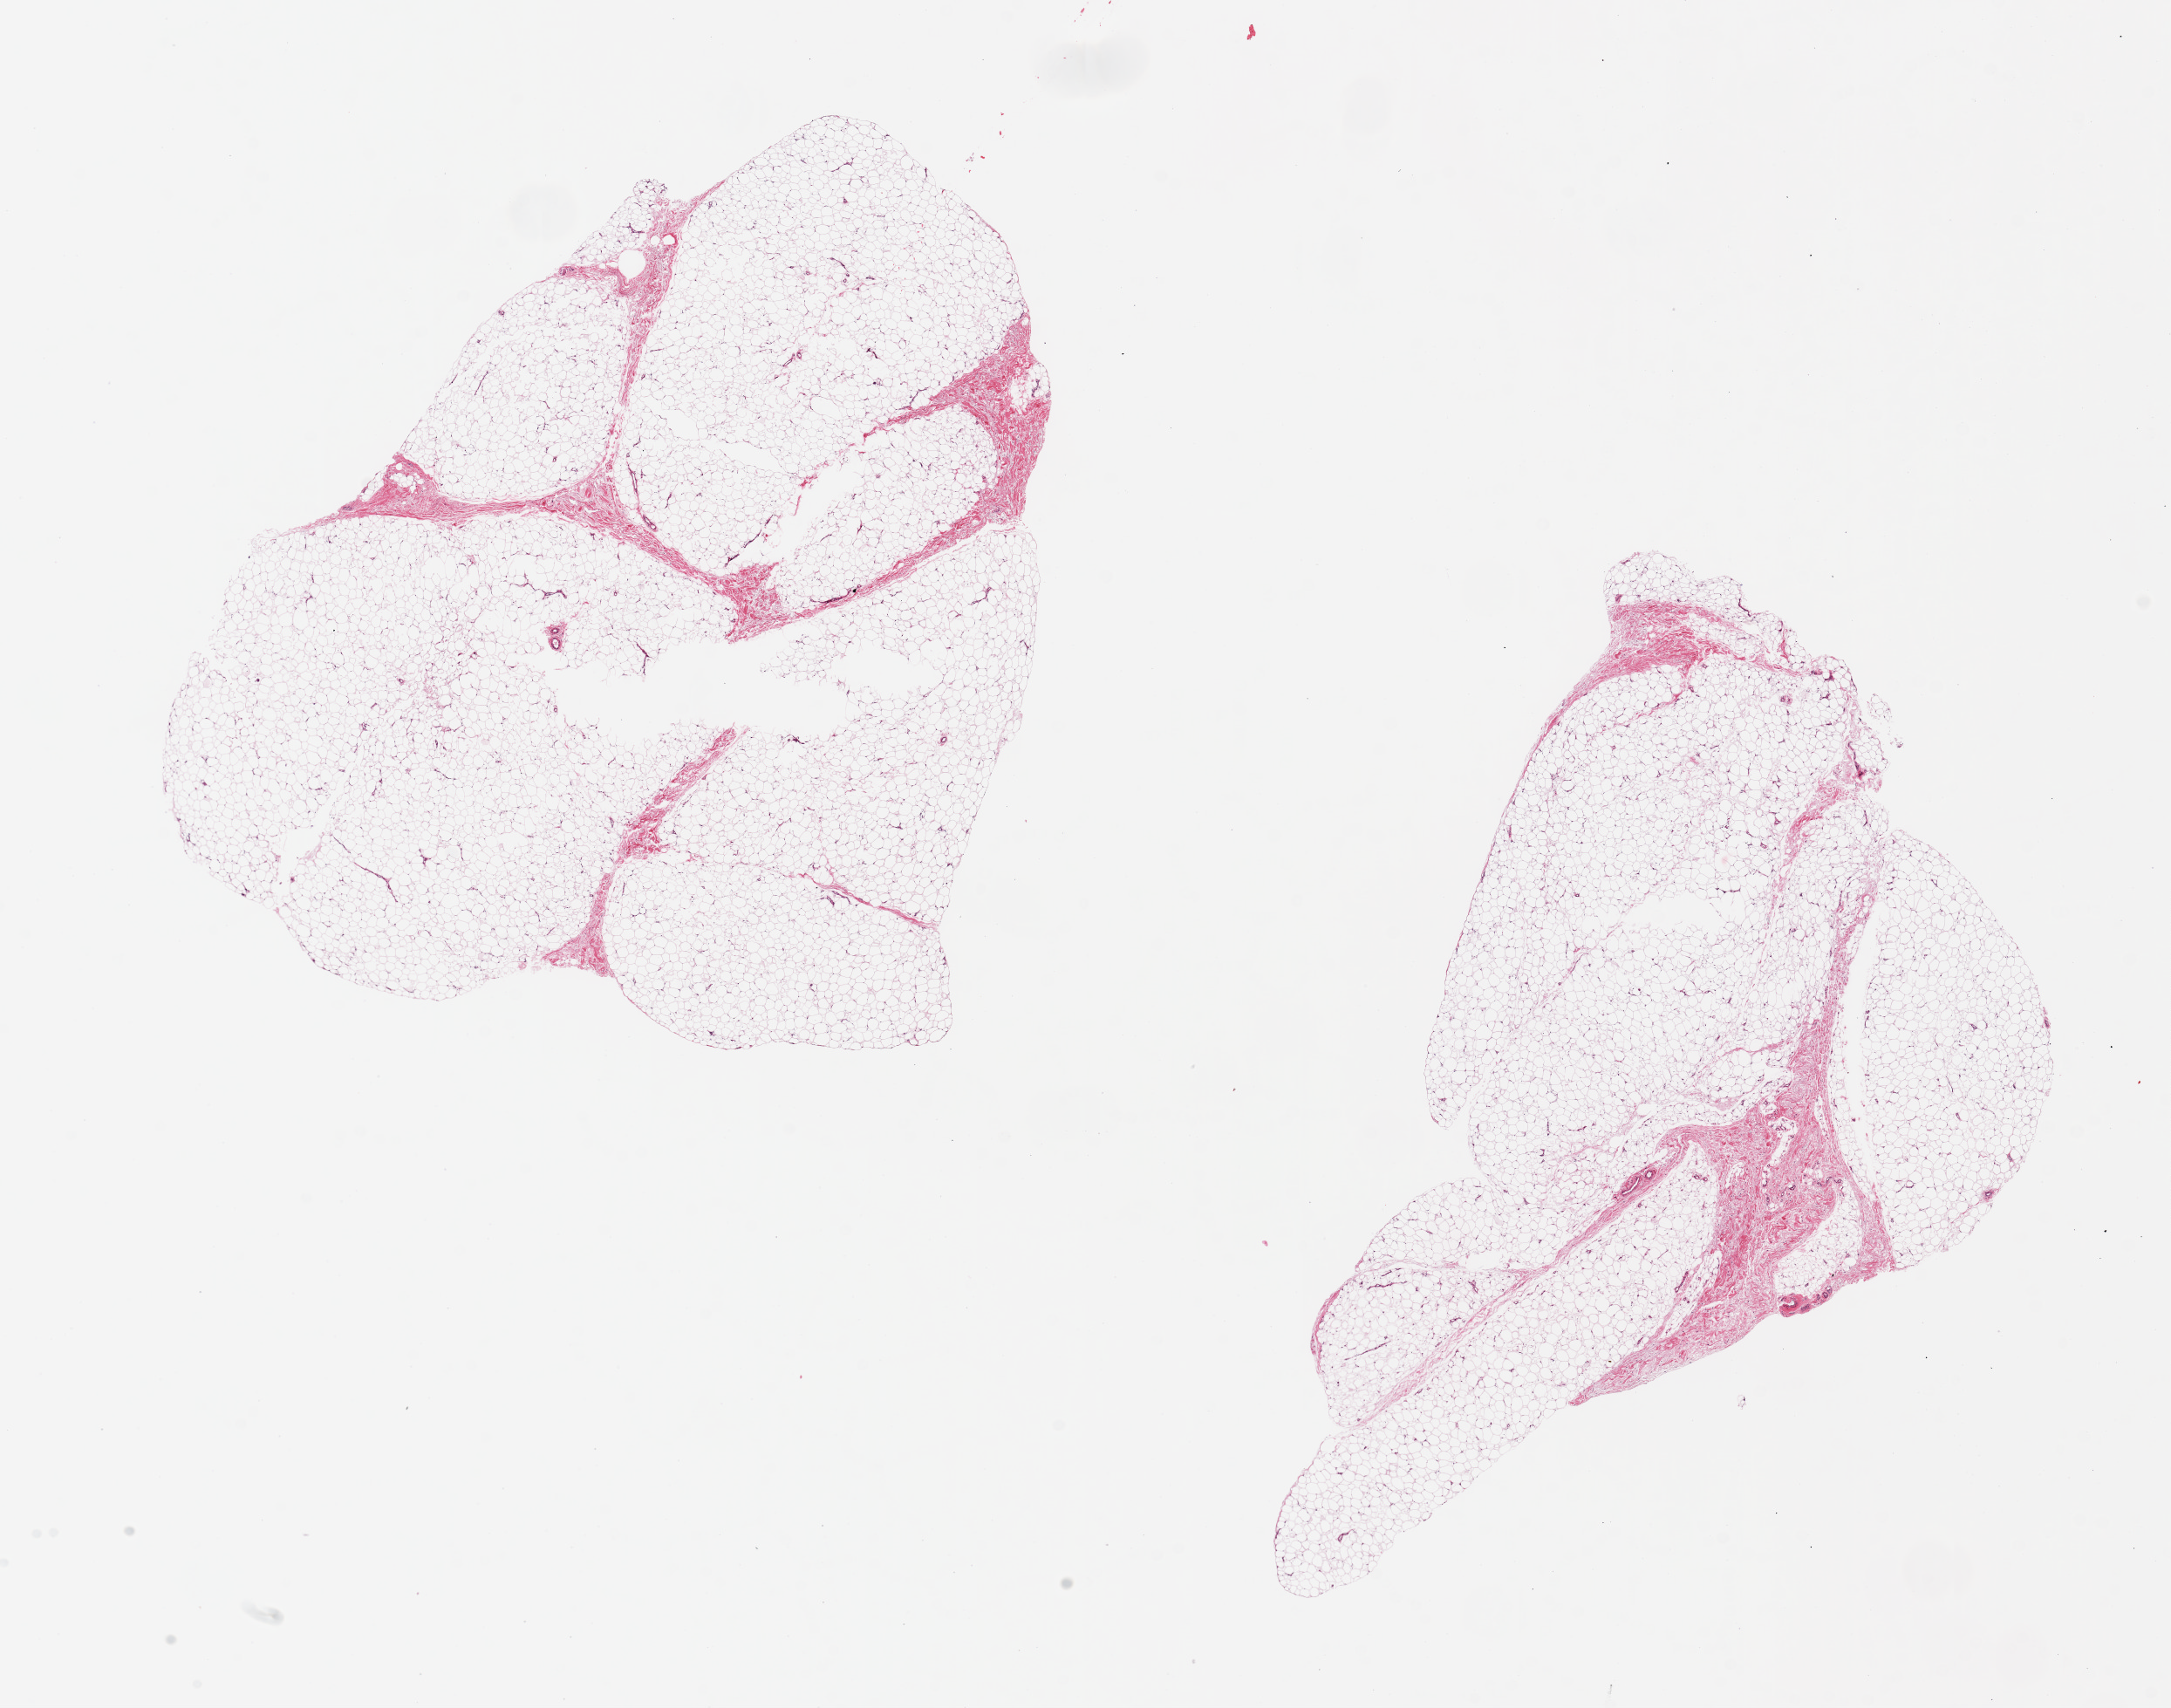
Digitized haematoxylin and eosin-stained section, low-resolution overview of the scanned area, about 19.7 x 15.5 mm, PAXgene-fixed paraffin-embedded (PFPE) section, section of adipose tissue (target tissue), tissue donor sample. Donor sex: male.
Pathologist's review note for this sample: 2 pieces, 9x8 & 10x8mm; Only small central 'unfixed' holes. Otherwise good specimen.